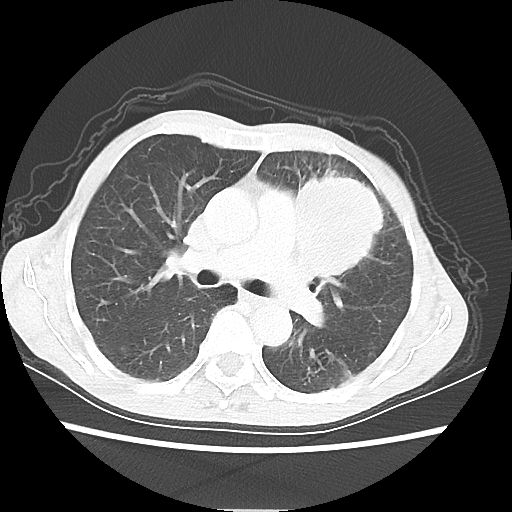
Chest CT, one axial slice. Slice 36 of 56 in the series (ordered by position). 80 kVp. Lung window (W 1500 / L -600 HU). 512 × 512 image matrix, field of view 331 × 331 mm. Patient: female, 60 years. Case-level facts recorded for this patient, not image findings: clinical TNM (as recorded): T4 N1 M0.
Outlined on this slice (rectangle marked by the reading radiologist):
- lung tumour (recorded histology: adenocarcinoma): bounding box [x1, y1, x2, y2] px = [293, 174, 387, 289]